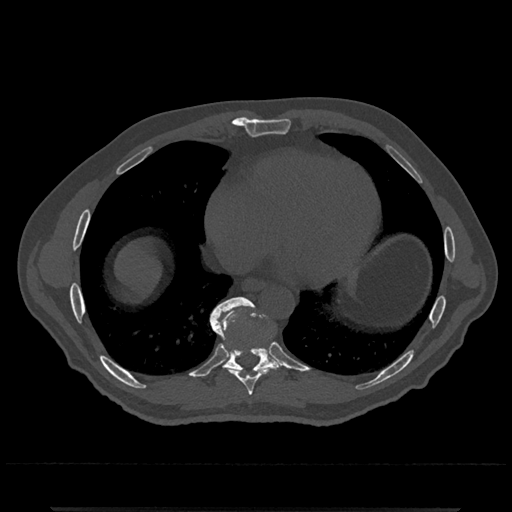
CT including the spine, one axial slice. Slice 642 of 797 in the series (ordered by position). Reconstruction kernel Br40s/3. 120 kVp. Bone window (W 1800 / L 400 HU). 512 × 512 image matrix, field of view 393 × 393 mm. Male patient, age 67 years. Case-level facts recorded for this patient, not image findings: primary cancer: prostate.
Outlined on this slice (semi-automatically segmented with operator editing):
- T8 vertebra: bounding box <212,326,281,396> (left, top, right, bottom; pixels)
- T9 vertebra: <210,297,280,375>